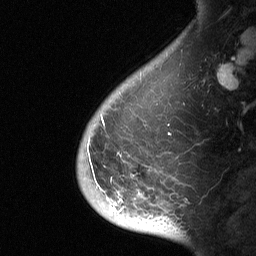
Breast MRI (dynamic contrast-enhanced), one sagittal slice; position 10 of 64 along the scan axis; dynamic contrast-enhanced study with each time point stored as its own series, time point 2 of 3 at this slice position (early post-contrast, ordered by acquisition time); 1.5 T; TE 4.8 ms, TR 27 ms; 2 mm slice thickness; 256 × 256 image matrix. Female patient, age 56 years. From the clinical record (not read from this slice): setting: breast cancer imaged before/during neoadjuvant chemotherapy; receptor status: HER2-positive.
Outlined on this slice (semi-automatically segmented with operator editing):
- analysis volume of interest (the breast-tissue region the enhancement analysis was run in; not a lesion): bounding box <76,104,182,229> (left, top, right, bottom; pixels)
- tumour enhancement mask (voxels above the 90 % enhancement threshold inside the analysis volume of interest): <115,154,141,204>